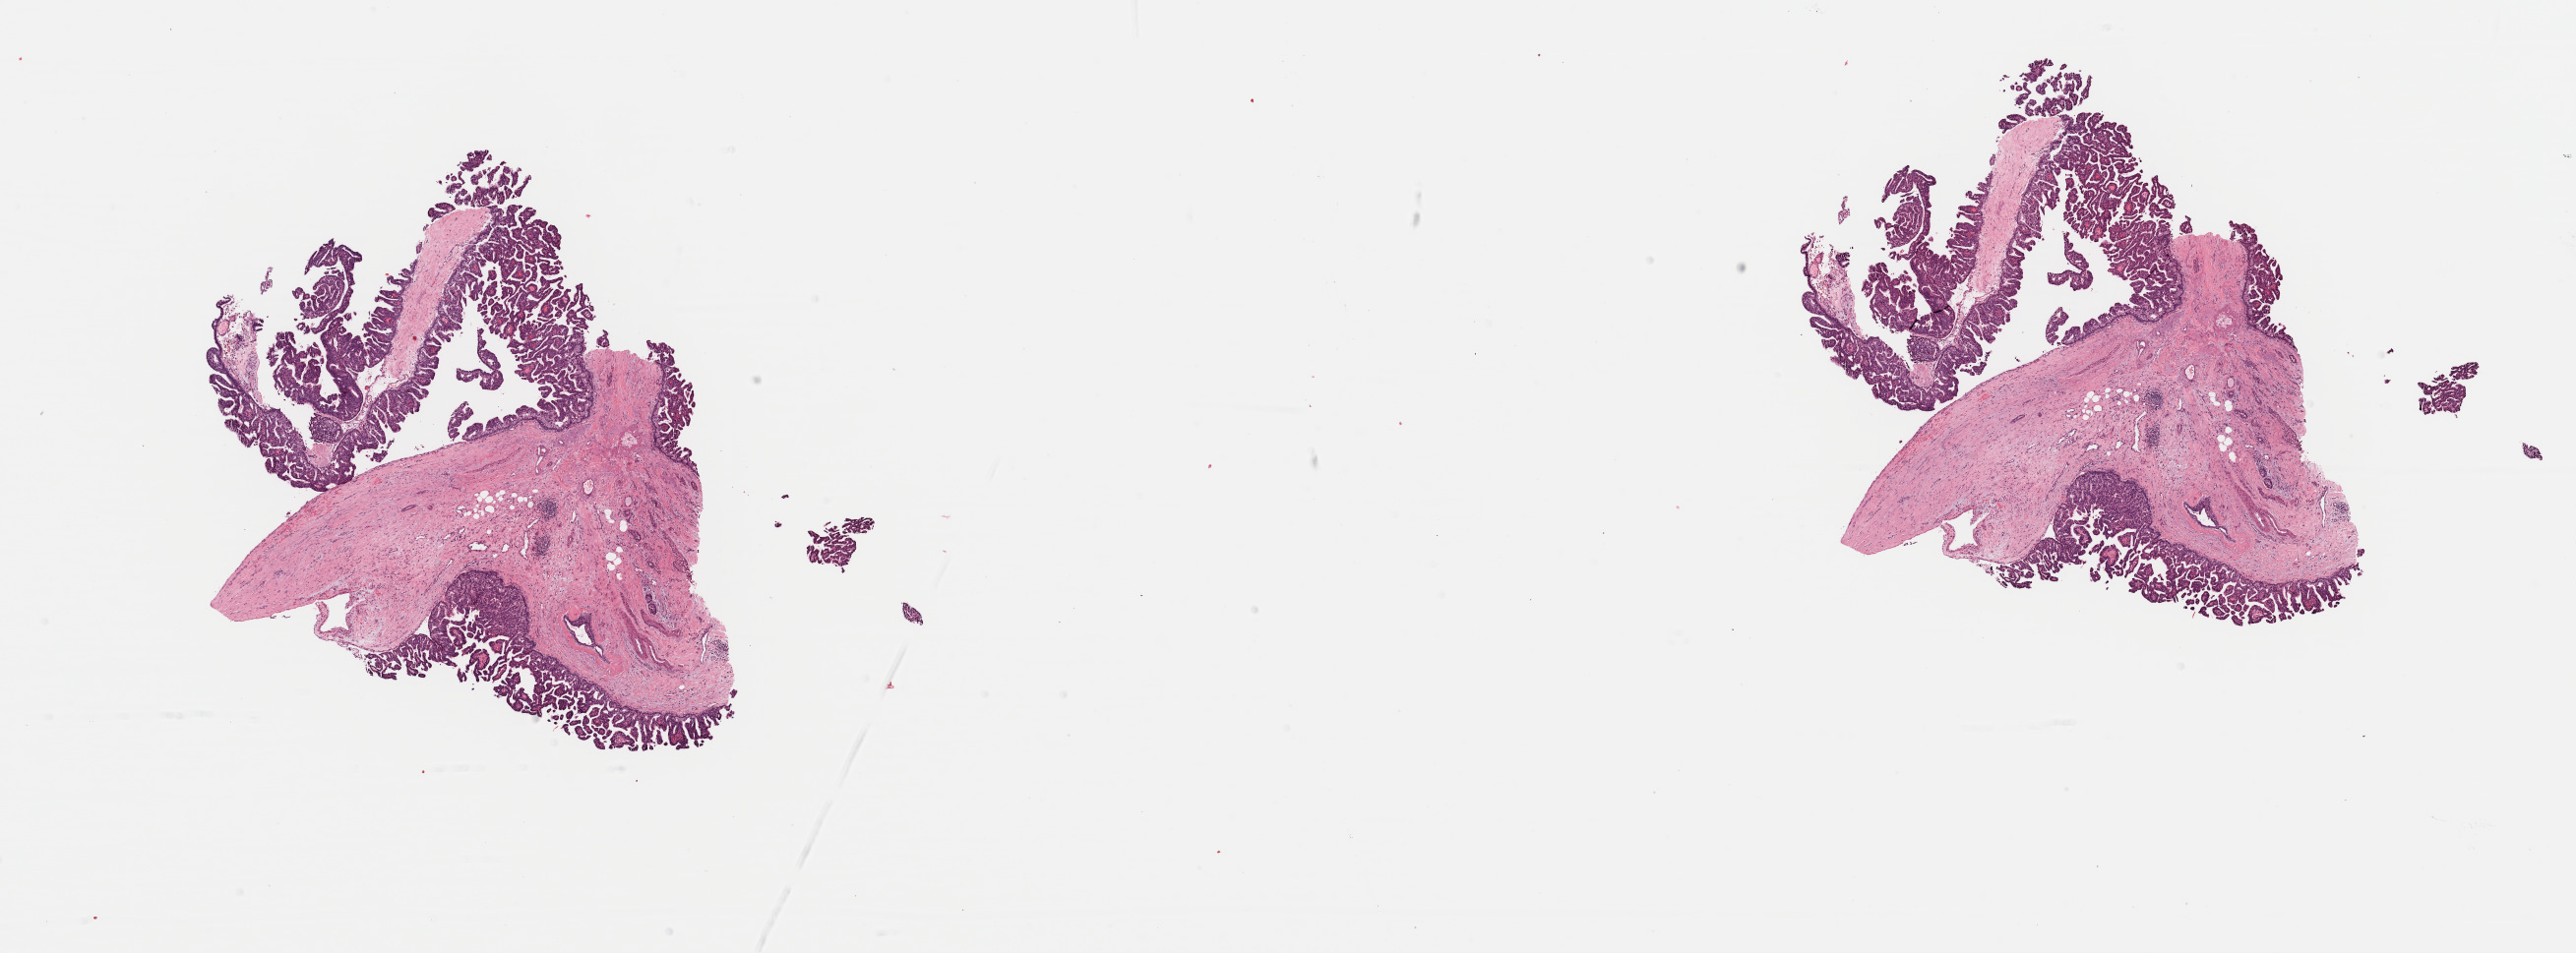
Whole-slide histology image, H&E, low-resolution overview of the scanned area, about 20.7 x 7.7 mm (slide scanned at 40x), FFPE section, breast, primary tumour sample. Female, age 63 years at initial diagnosis.
Diagnosis: Infiltrating duct carcinoma, NOS. AJCC pathologic stage: IA.